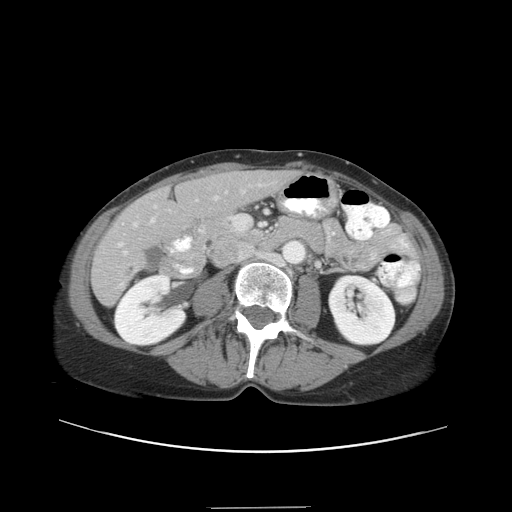
Contrast-enhanced abdominal CT, one axial slice. Position 12 of 38 along the scan axis. Reconstruction kernel STANDARD. 120 kVp. Intravenous contrast given. Soft-tissue window (W 400 / L 40 HU). 5 mm slice thickness. 512 × 512 image matrix. Female patient, age 64 years. Case-level facts recorded for this patient, not image findings: diagnosis: colorectal cancer liver metastases, imaged before liver resection; multiple liver metastases: no; largest metastasis: 3.8 cm.
Annotated regions visible in this slice (expert manual segmentation):
- hepatic veins: bounding box (x1, y1, x2, y2) in pixels: (118, 190, 245, 247)
- liver: (93, 171, 294, 303)
- planned liver remnant (the part of the liver to remain after resection): (152, 171, 294, 227)
- portal vein (with intrahepatic branches): (123, 191, 228, 255)